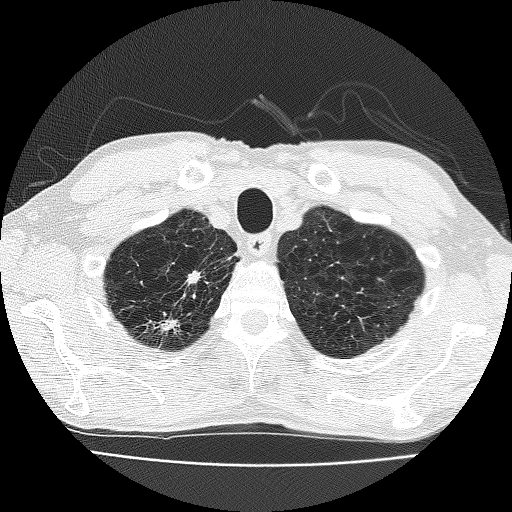
Low-dose screening chest CT, one axial slice; slice 155 of 185 in the series (ordered by position); reconstruction kernel FC51; 120 kVp; lung window (W 1500 / L -600 HU); 512 × 512 image matrix, field of view 322 × 322 mm.
Outlined on this slice (expert manual segmentation):
- lesion 1 (nodule, upper lobe of right lung): box from (x=187, y=271) to (x=200, y=284) px
- lesion 2 (nodule, upper lobe of right lung): (x=157, y=317)–(x=180, y=331)